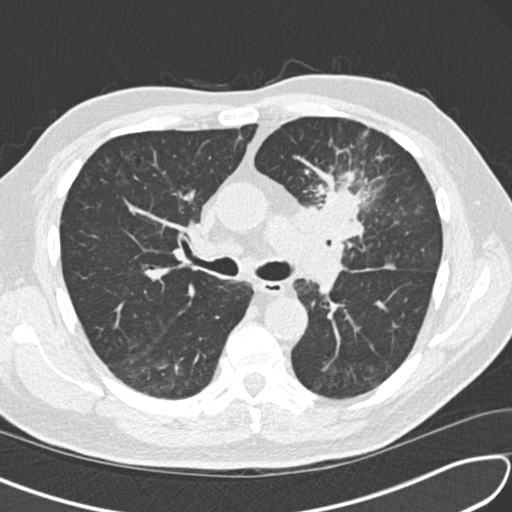
Low-dose screening chest CT, one axial slice; slice 96 of 156 in the series (ordered by position); 120 kVp; lung window (W 1500 / L -600 HU); 2 mm slice thickness; 512 × 512 image matrix, field of view 340 × 340 mm.
Outlined on this slice (manually delineated by an expert):
- lesion 1 (tumor, upper lobe of left lung): bounding box (x1, y1, x2, y2) in pixels: (317, 190, 362, 240)